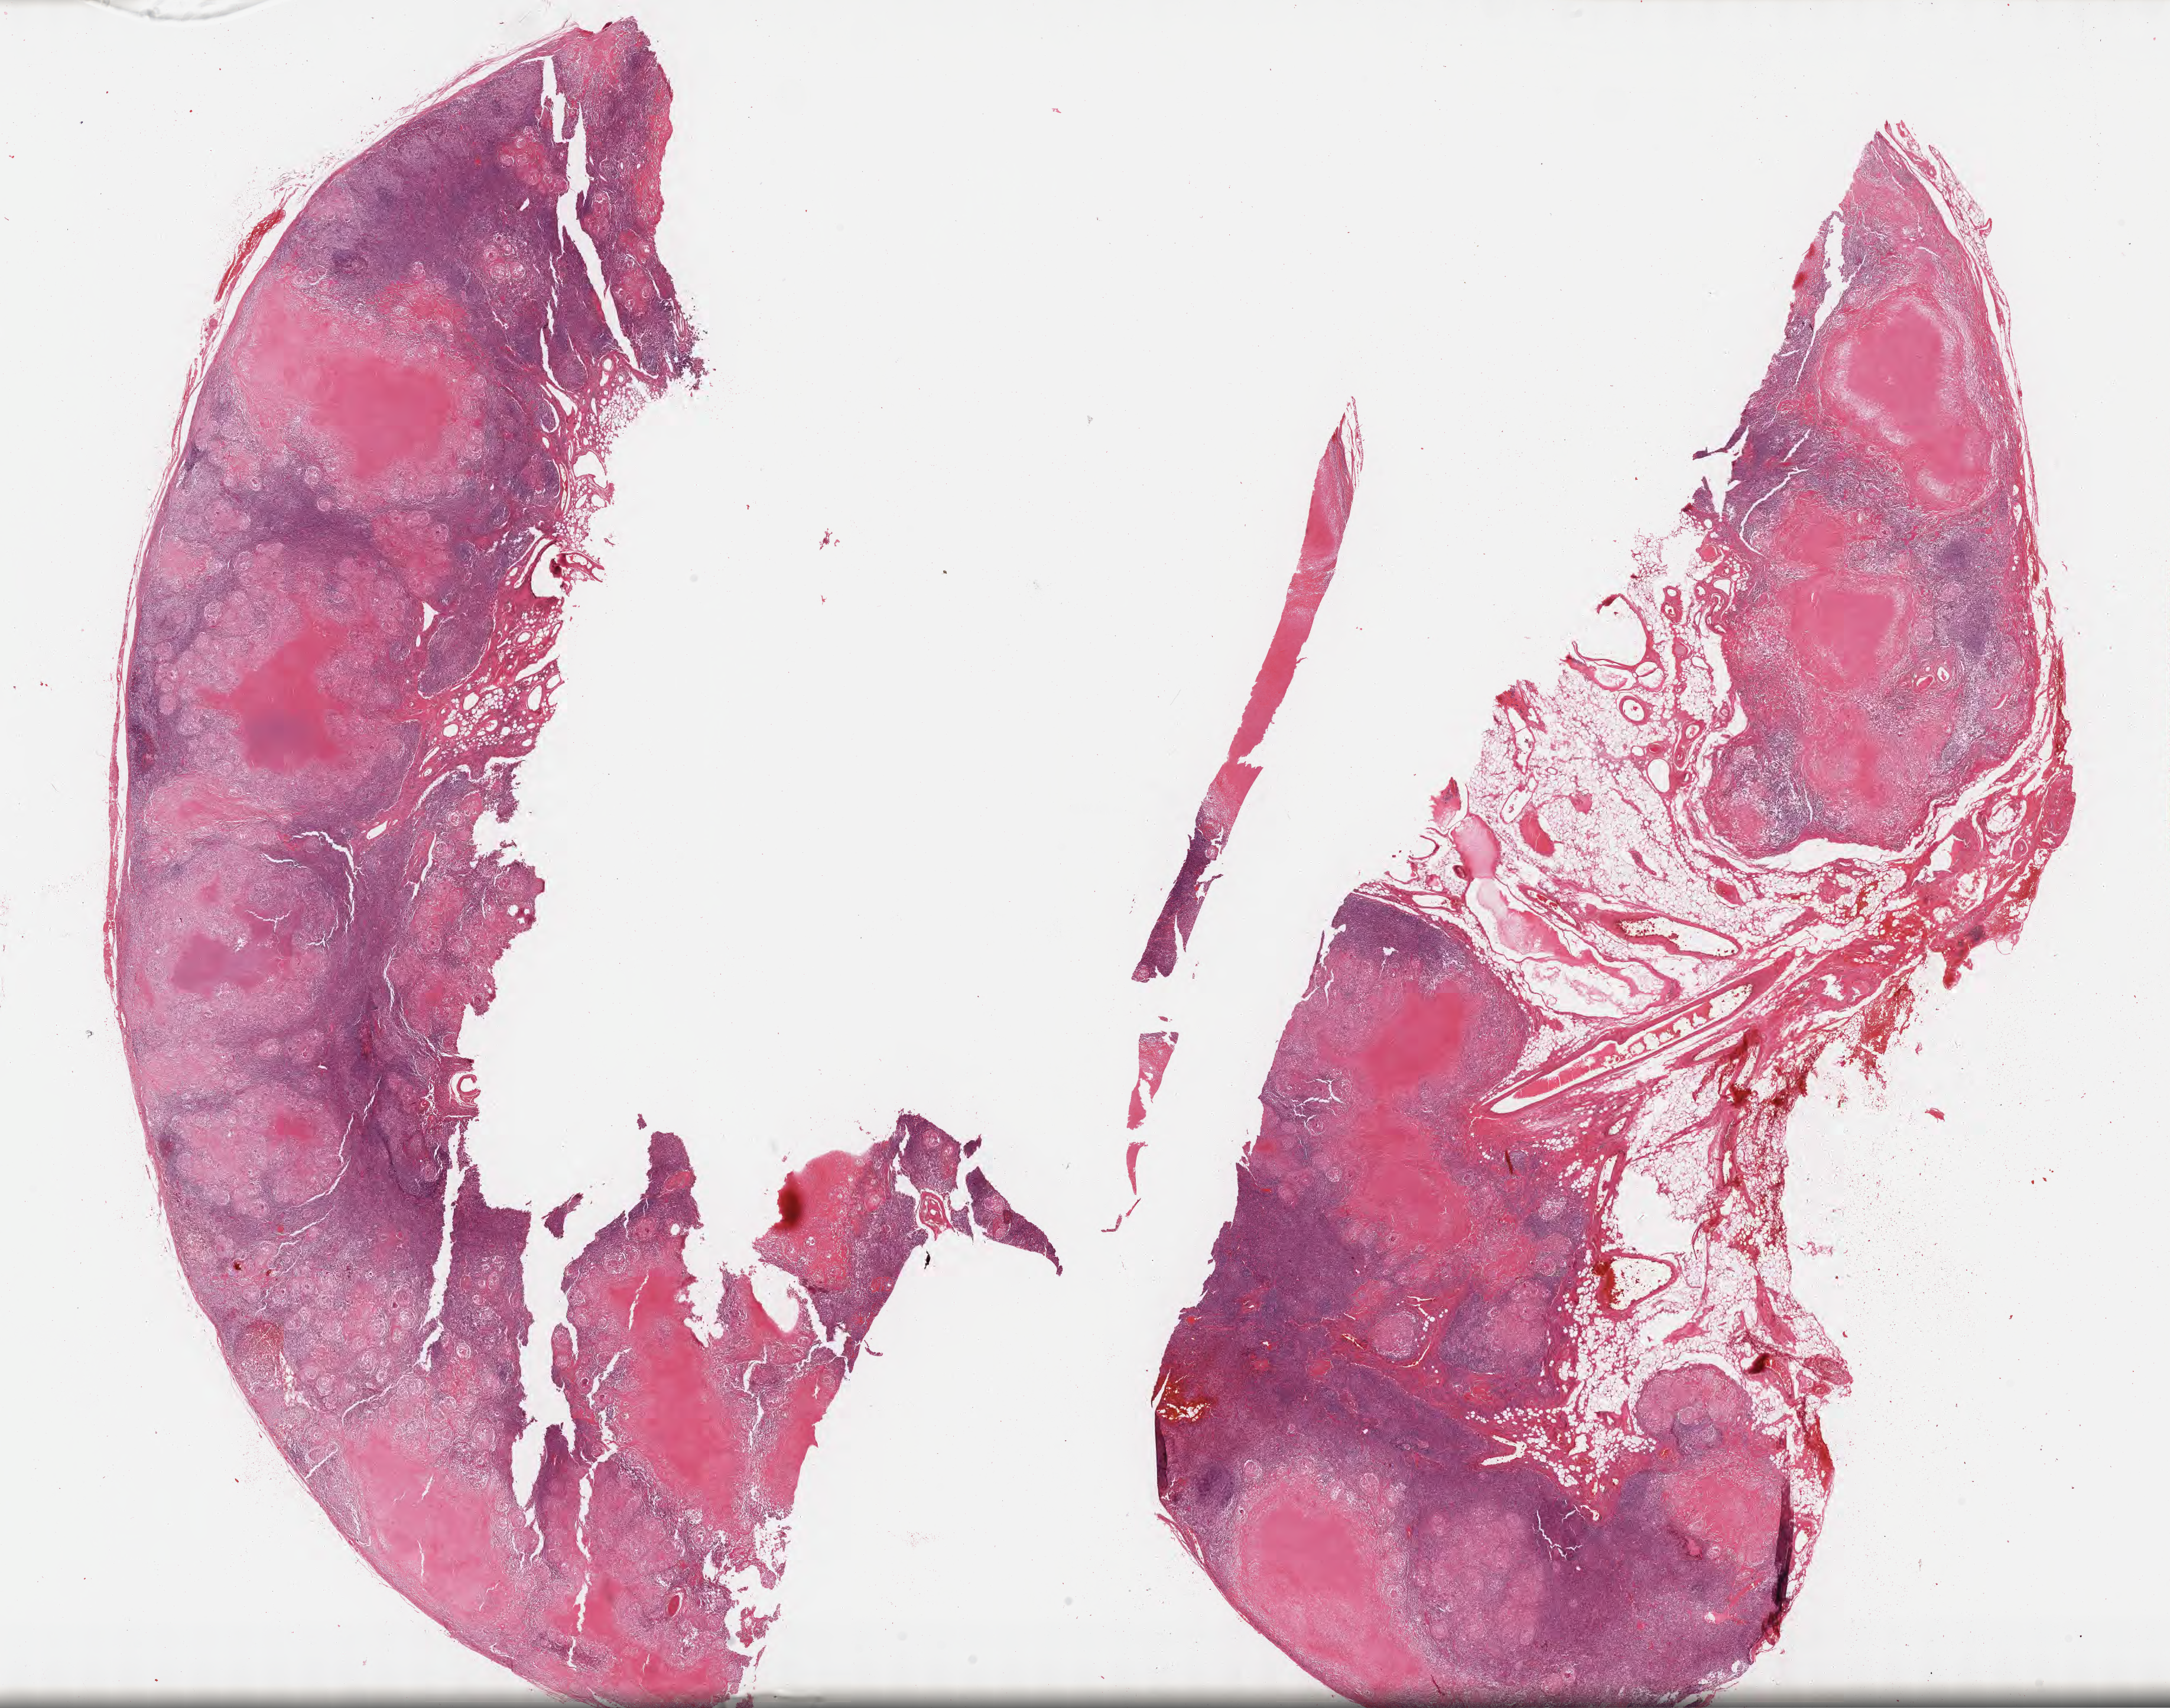
H&E whole-slide image — a low-resolution overview of the entire scanned area, about 29.7 x 23.4 mm, FFPE section, normal-tissue sample (non-tumor) from a patient with burkitt lymphoma, NOS. Patient male; aged 46. Composition of this section per pathologist review: tumor cells 0%, tumor nuclei 0%, stromal cells 20%, necrosis 40%, normal cells 40%. Infiltration values recorded for this section: lymphocyte infiltration 75%, monocyte infiltration 15%, neutrophil infiltration 5%.
This section: non-tumor tissue sample; the patient's diagnosis is given above.